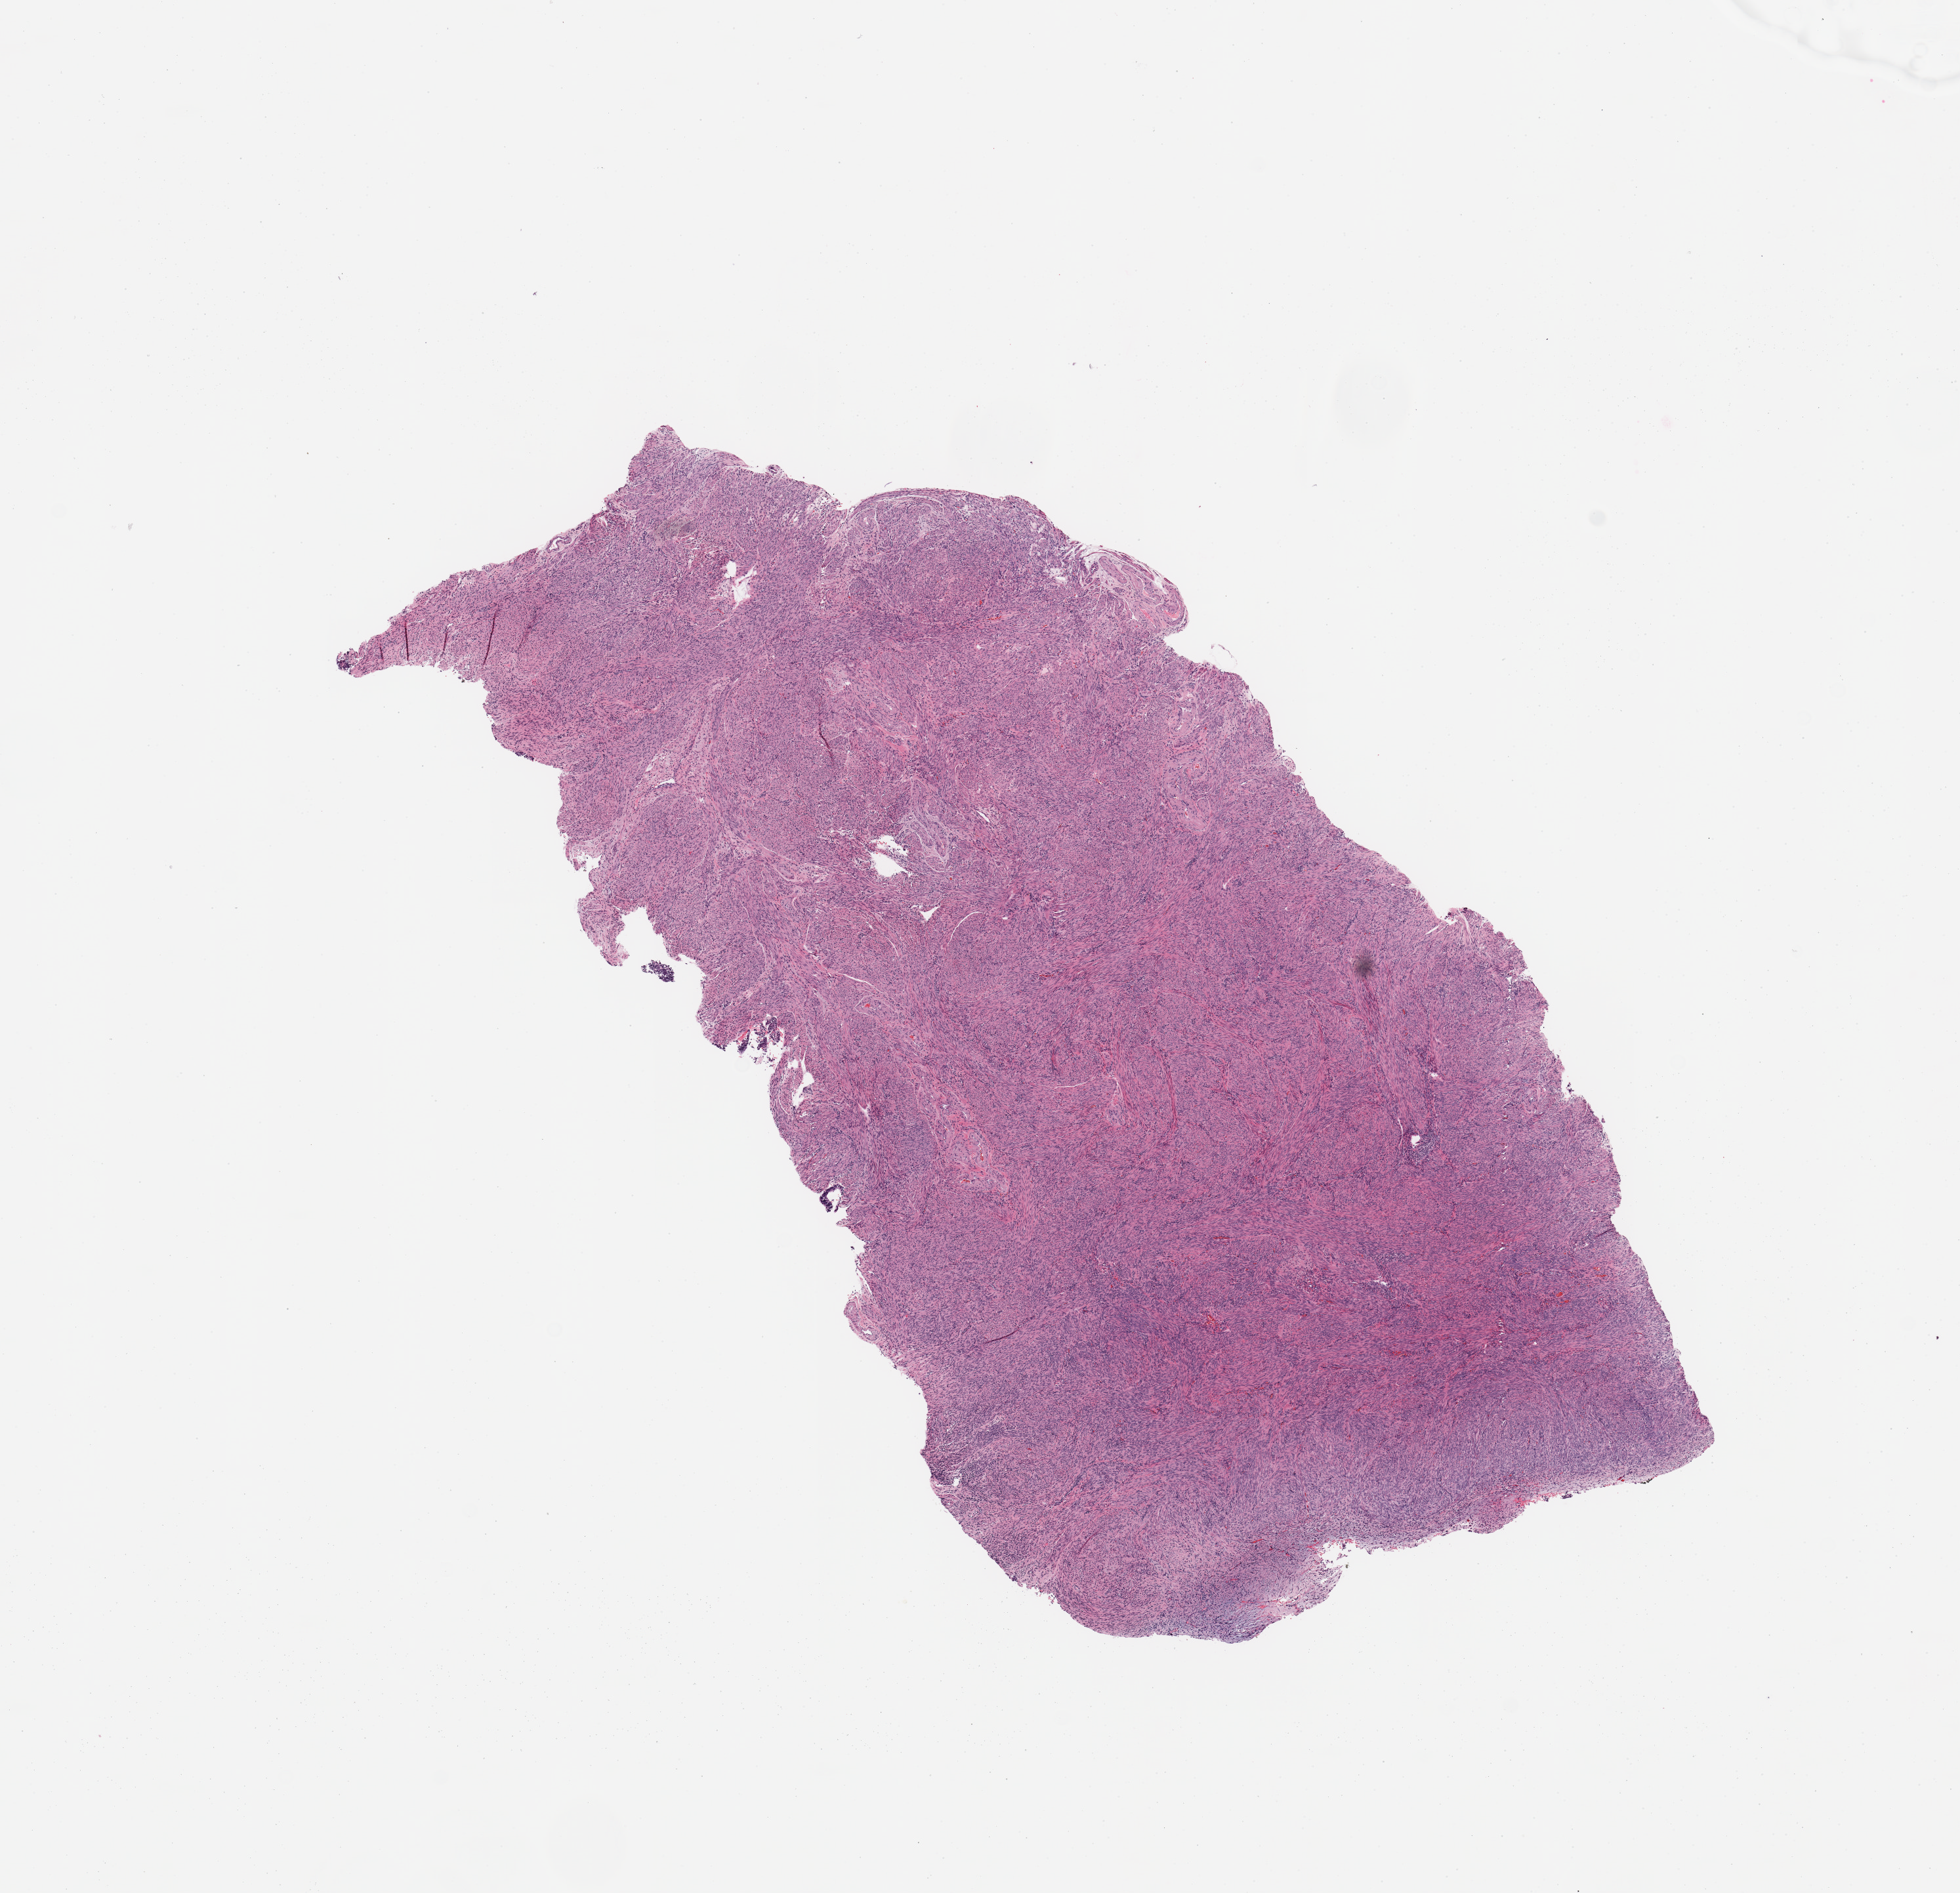
Whole-slide histology image, H&E, a low-resolution overview of the entire scanned area, about 11.8 x 11.4 mm, uterus, normal (non-tumour) tissue. 75-year-old female patient.
This section: normal (non-tumour) tissue from the same patient. Patient diagnosis: Endometrioid adenocarcinoma, NOS.